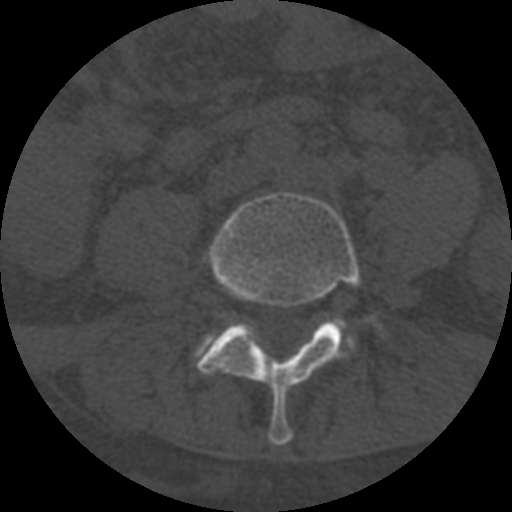
CT including the spine, one axial slice; position 203 of 708 along the scan axis; reconstruction kernel STANDARD; one of 3 acquisitions stored at this slice position; bone window (W 1800 / L 400 HU); 512 × 512 image matrix, field of view 160 × 160 mm. Patient age 55 years. Case-level facts recorded for this patient, not image findings: primary cancer: colon.
Annotated regions visible in this slice (semi-automatically segmented with operator editing):
- L4 vertebra: box from (x=197, y=192) to (x=375, y=446) px
- L5 vertebra: (x=210, y=318)–(x=355, y=345)